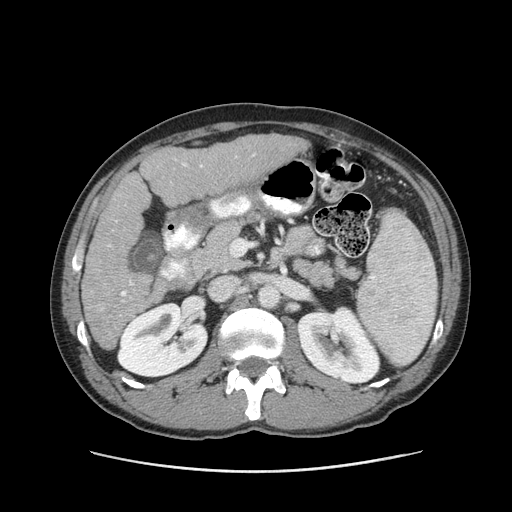
Contrast-enhanced abdominal CT (liver protocol), one axial slice. Position 42 of 93 along the scan axis. Reconstruction kernel STANDARD. Soft-tissue window (W 400 / L 40 HU). 2.5 mm slice thickness. 512 × 512 image matrix. From the clinical record (not read from this slice): diagnosis: hepatocellular carcinoma (patient treated with transarterial chemoembolisation; whether this scan precedes or follows treatment is not stated here); TNM stage (as recorded): Stage-II; Child-Pugh class: A; tumour differentiation: moderately differentiated; tumour nodularity: multinodular.
Annotated regions visible in this slice (semi-automatic segmentation, software-assisted and operator-edited):
- liver parenchyma outside the tumour (the mass and vessels are separate outlines, so this box may not span the whole liver): bounding box [x1, y1, x2, y2] px = [82, 134, 308, 350]
- liver vessels: [108, 154, 255, 296]